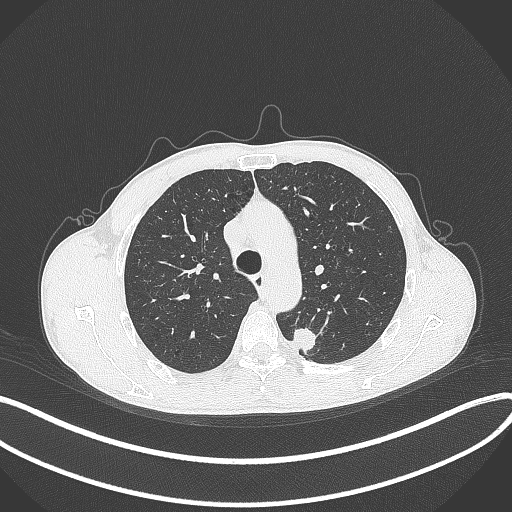
Chest CT, one axial slice; position 289 of 429 along the scan axis; reconstruction kernel B70f; lung window (W 1500 / L -600 HU); 1 mm slice thickness; 512 × 512 image matrix, field of view 400 × 400 mm. Patient: male, 51 years. From the clinical record (not read from this slice): clinical TNM (as recorded): T2a N1 M1.
Annotated regions visible in this slice (rectangle marked by the reading radiologist):
- lung tumour (recorded histology: adenocarcinoma): box from (x=293, y=324) to (x=317, y=356) px